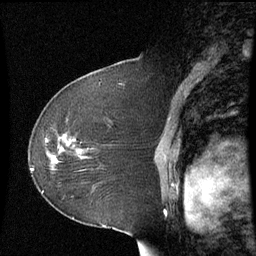
Breast MRI (dynamic contrast-enhanced), one sagittal slice. Slice 39 of 60 in the series (ordered by position). Dynamic contrast-enhanced series, image 2 of 3 at this slice position (ordered by acquisition). 1.5 T. TE 4.2 ms, TR 8.9 ms. 256 × 256 image matrix, field of view 210 × 210 mm. Patient: female, 51 years. From the clinical record (not read from this slice): setting: breast cancer imaged before/during neoadjuvant chemotherapy; receptor status: HR-positive, HER2-negative.
Structures marked on this image (semi-automatic segmentation, software-assisted and operator-edited):
- analysis volume of interest (the breast-tissue region the enhancement analysis was run in; not a lesion): box from (x=50, y=138) to (x=88, y=174) px
- tumour enhancement mask (voxels above the 70 % enhancement threshold inside the analysis volume of interest): (x=67, y=143)–(x=71, y=145)